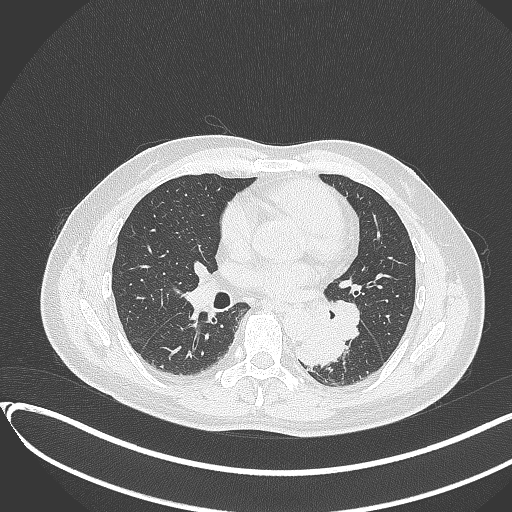
Chest CT, one axial slice; position 171 of 417 along the scan axis; 120 kVp; lung window (W 1500 / L -600 HU); 1 mm slice thickness; 512 × 512 image matrix, field of view 400 × 400 mm. Patient: male, 54 years. Case-level facts recorded for this patient, not image findings: clinical TNM (as recorded): T3 N0 M0.
Structures marked on this image (bounding box drawn by a radiologist):
- lung tumour (recorded histology: squamous cell carcinoma): bounding box [x1, y1, x2, y2] px = [294, 320, 351, 370]